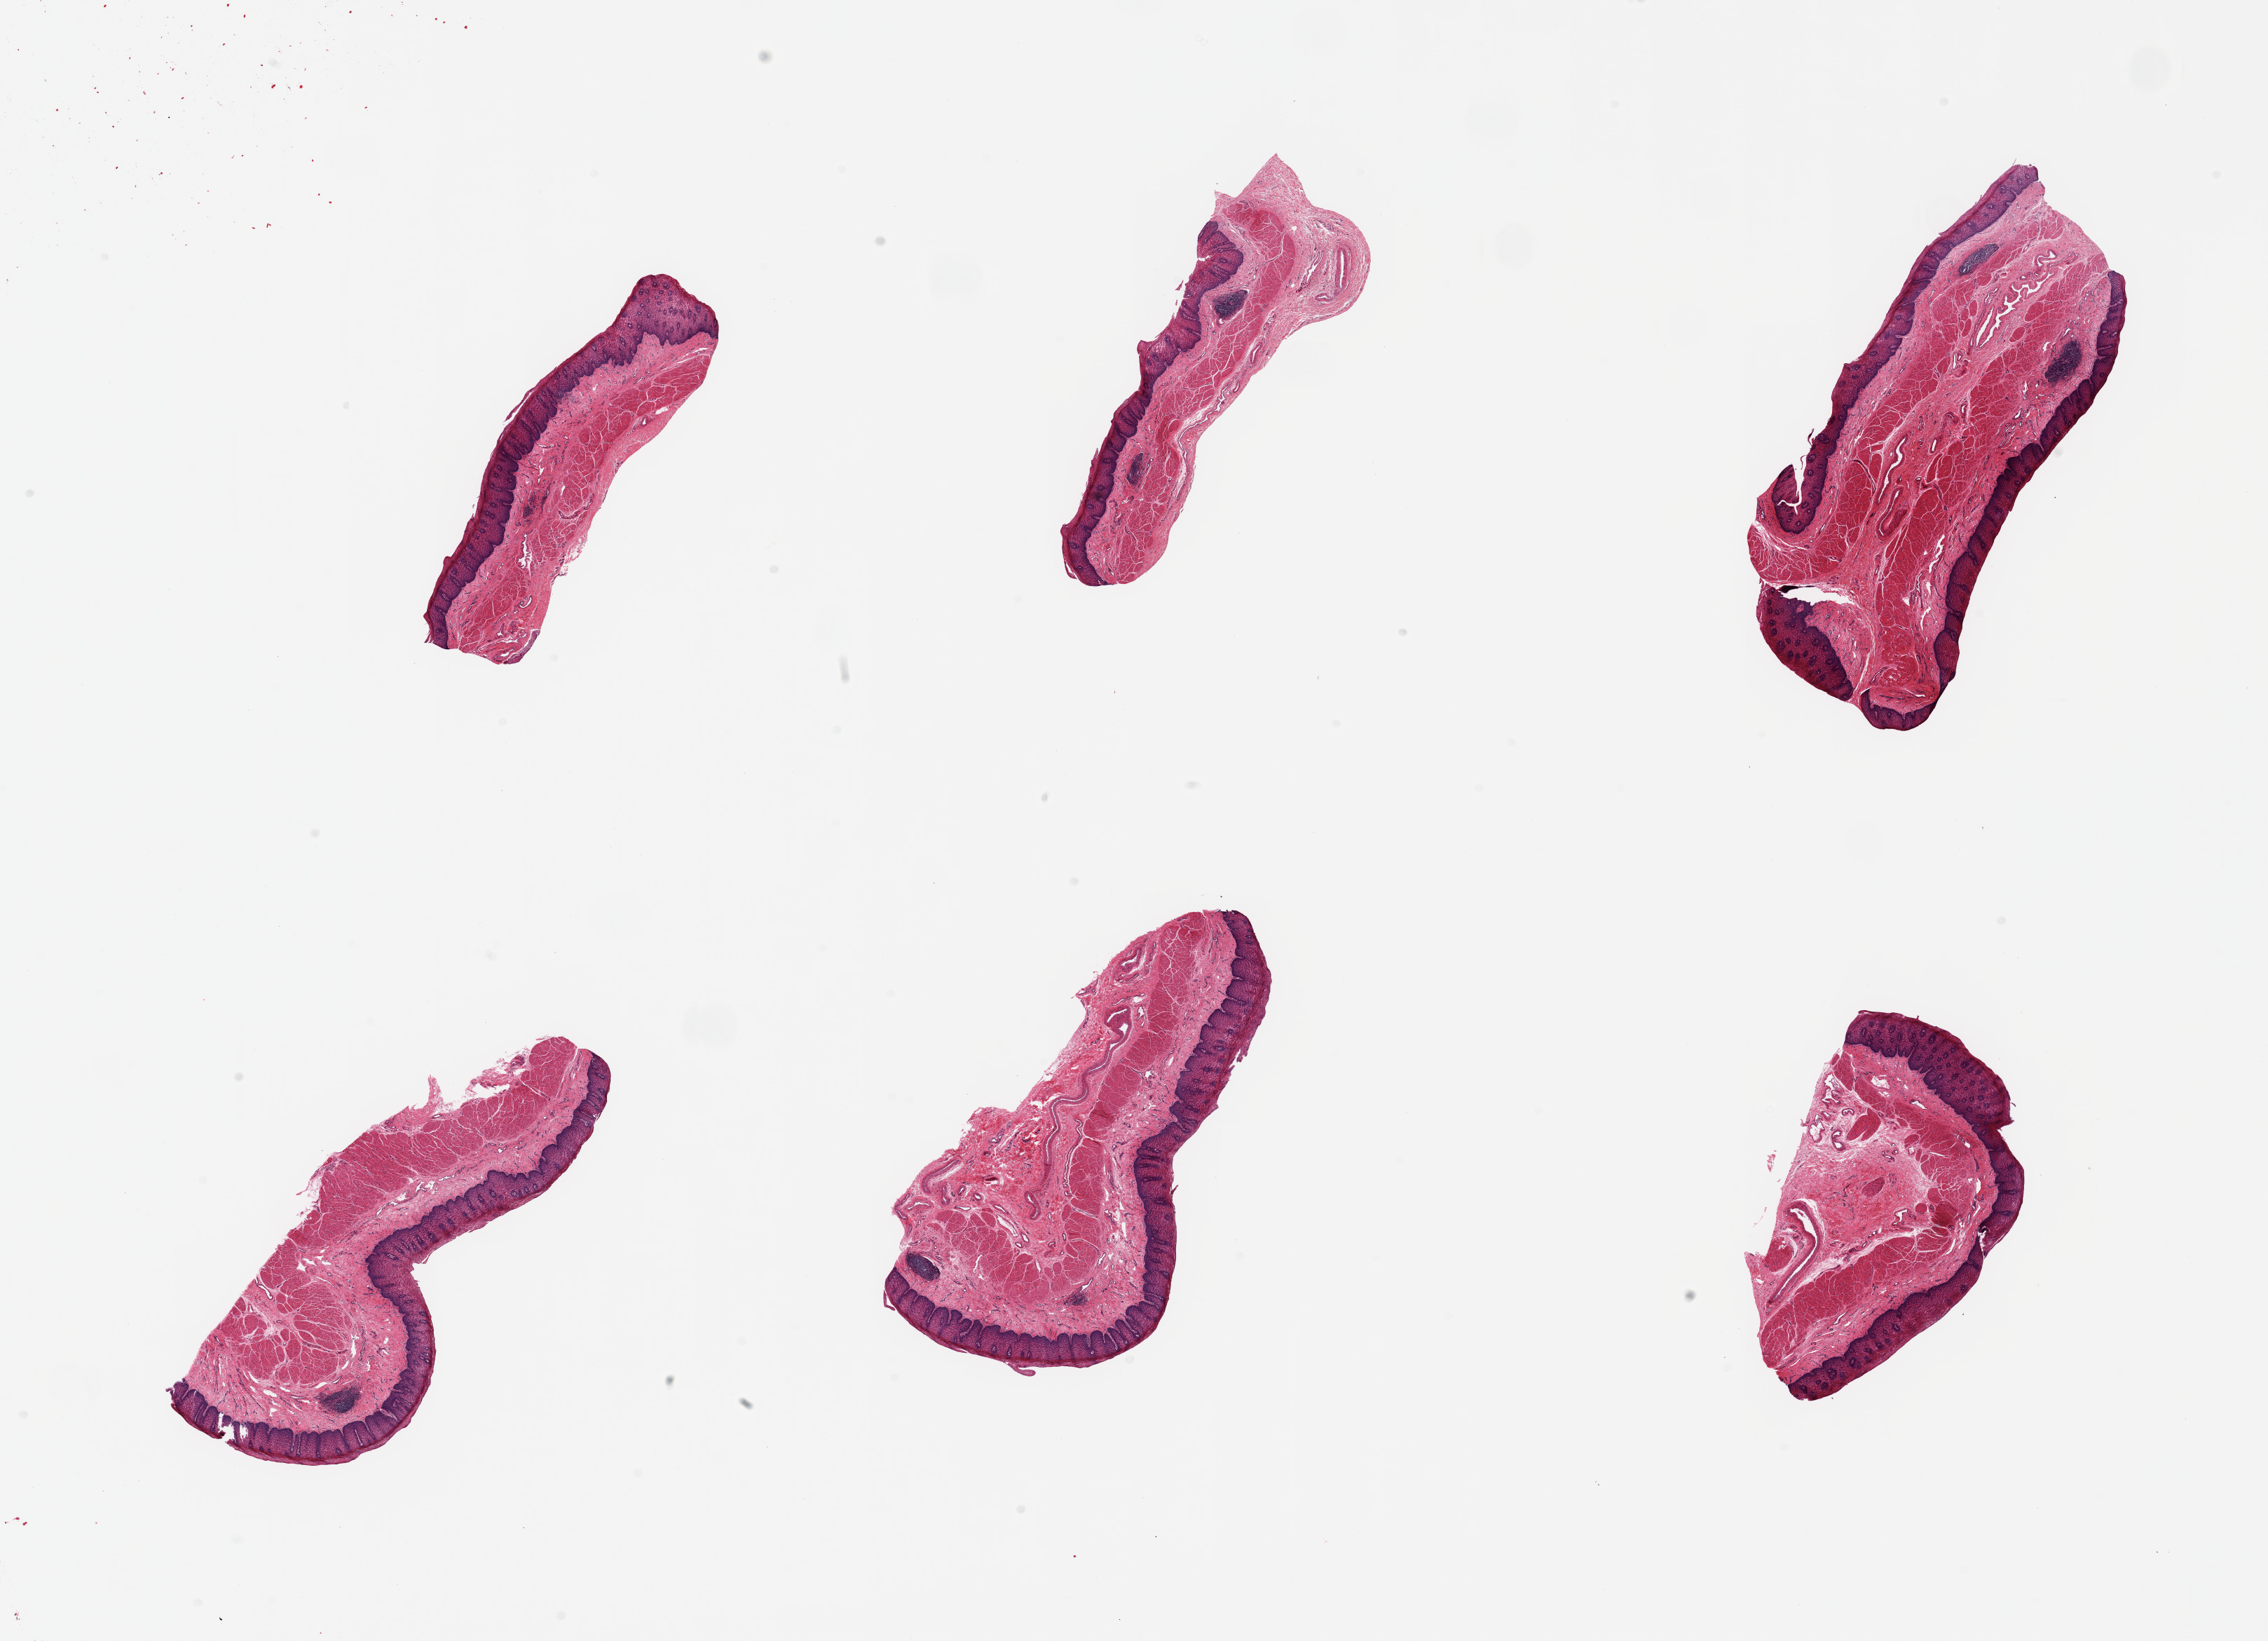
Whole-slide image, H&E stain — shown as a low-resolution overview of the whole scanned area (about 25.6 x 18.5 mm), PAXgene-fixed paraffin-embedded (PFPE) section, sampled site (target tissue): esophageal mucous membrane, tissue donor sample. Donor: male.
• pathologist's review note for this sample: 6 pieces, squamous mucosa up to ~0.5mm, 10-25% thickness